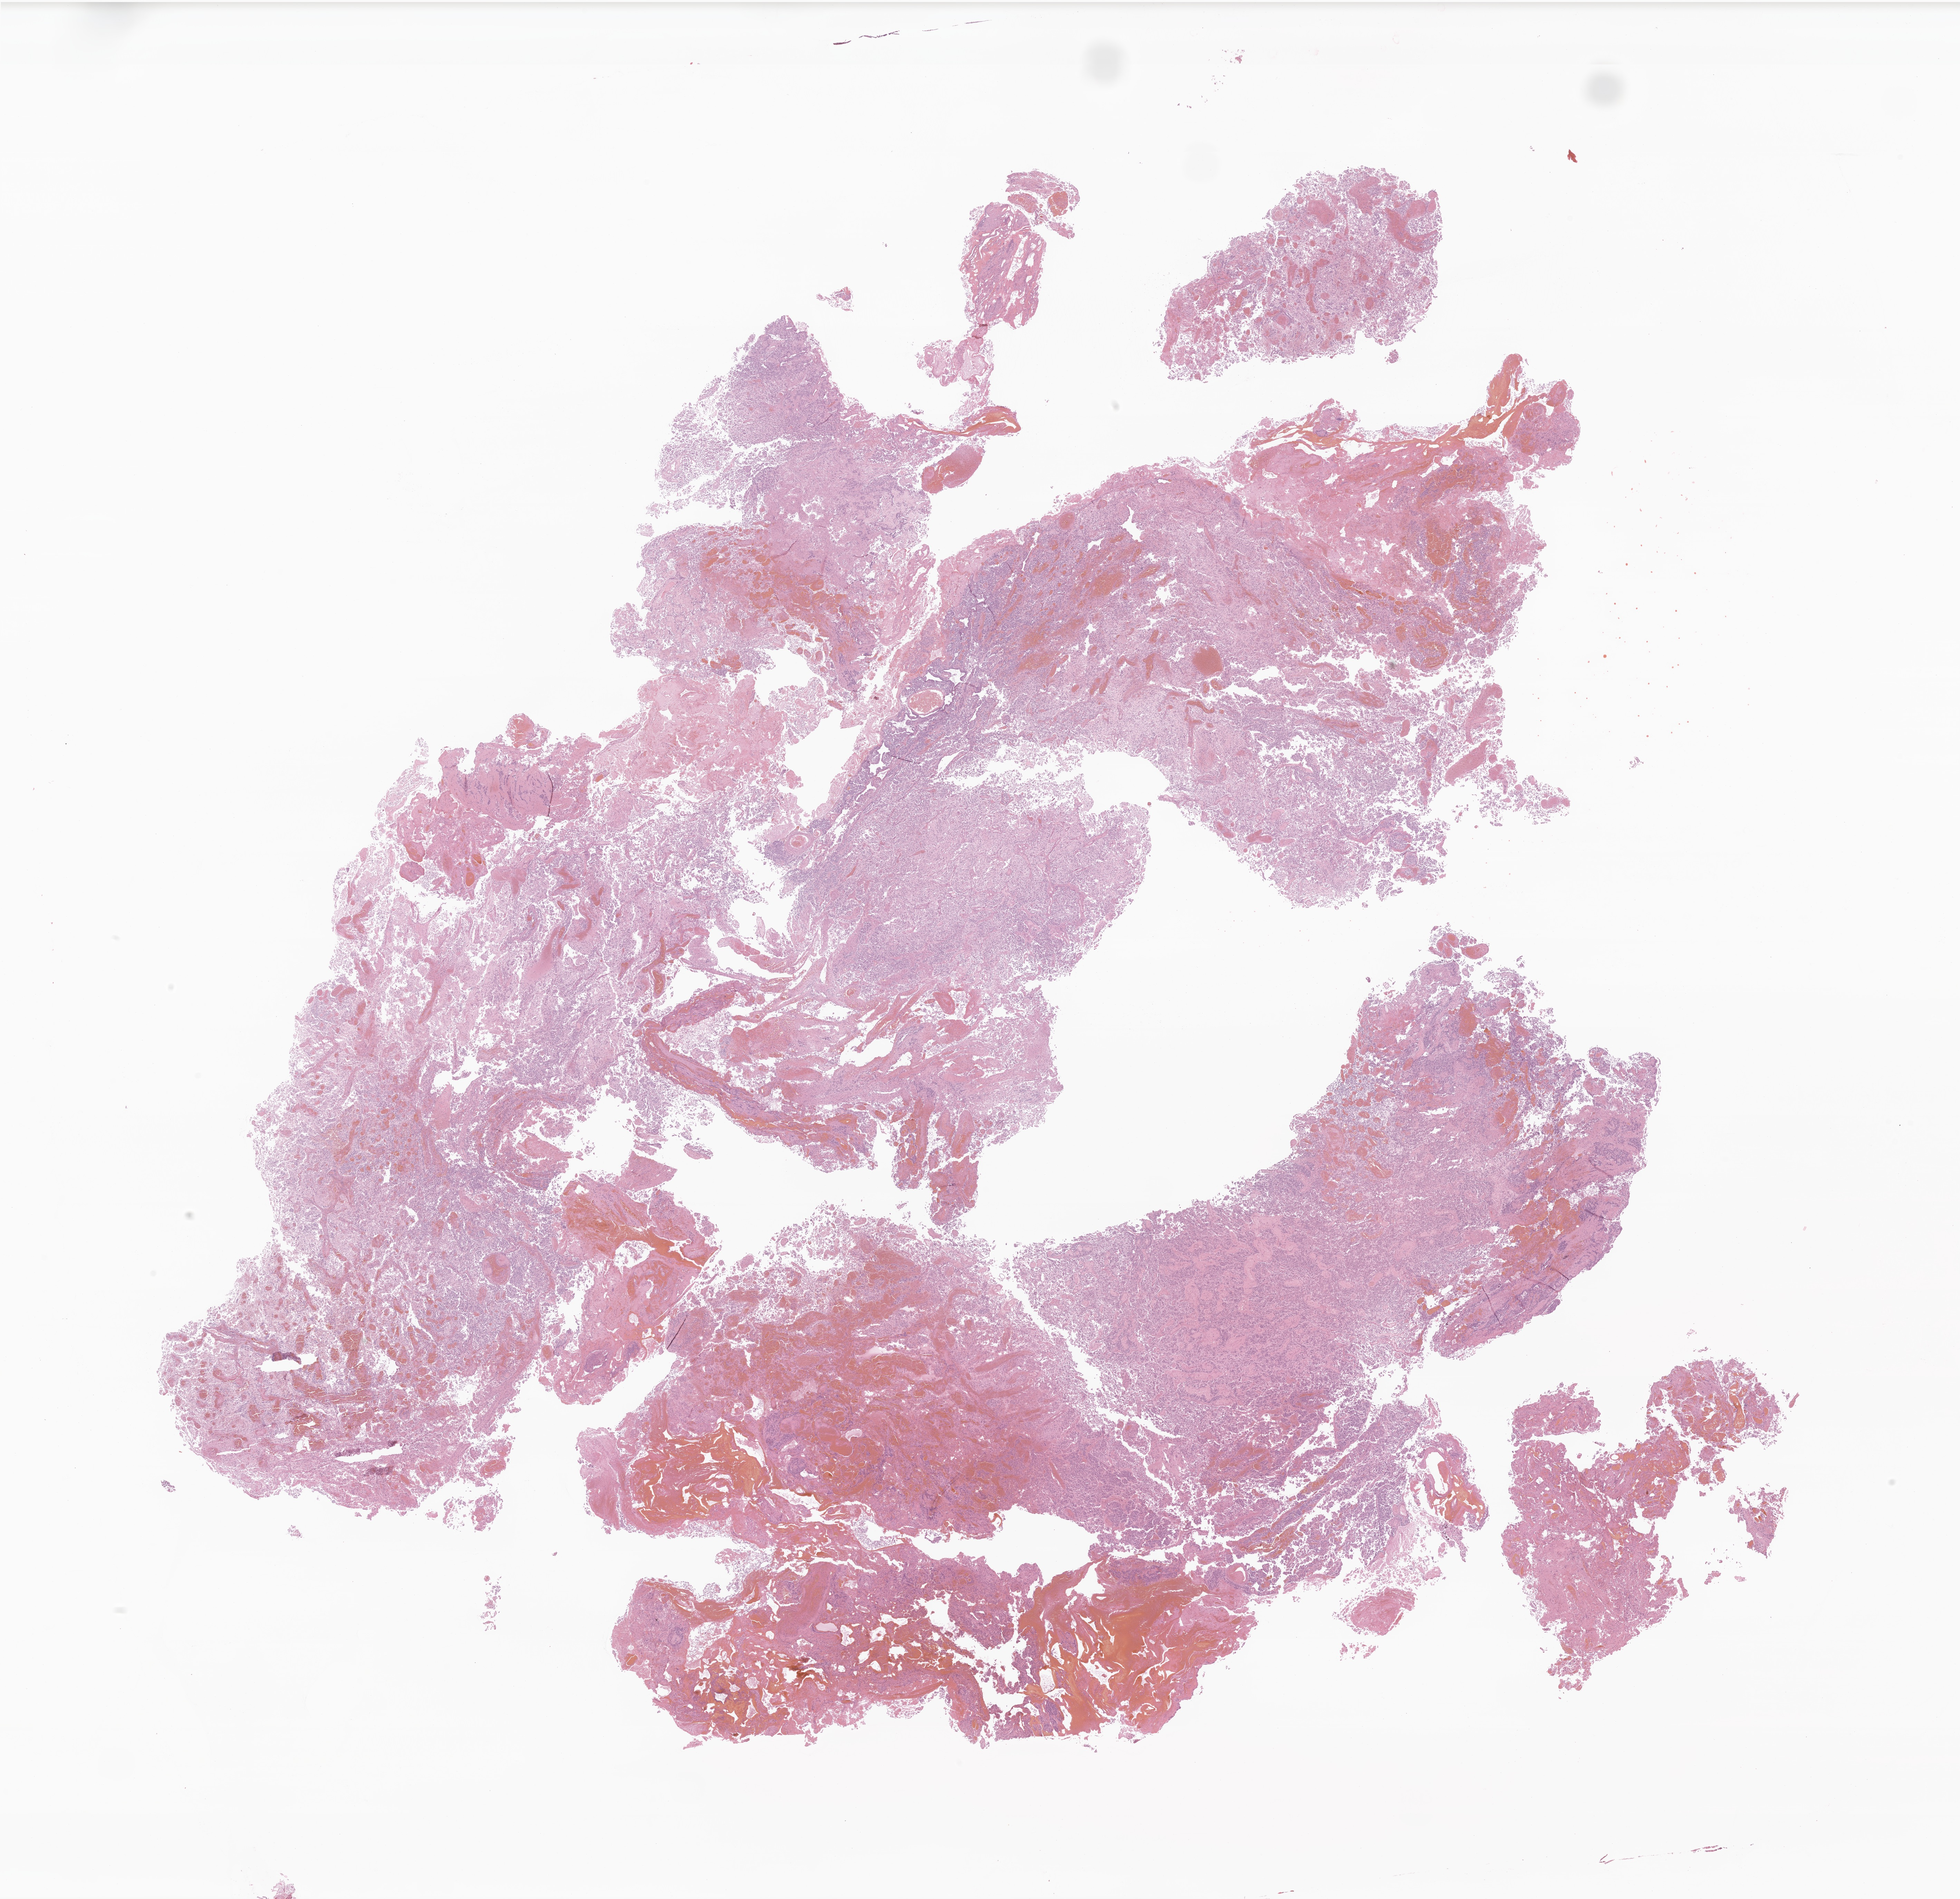
Whole-slide image, H&E stain of tumor tissue from the parietal lobe — low-resolution overview of the scanned area, about 23.9 x 23.2 mm; formalin-fixed, paraffin-embedded (FFPE) tissue. Patient: female, age 53 months.
Diagnosis: CNS embryonal tumor, NOS.